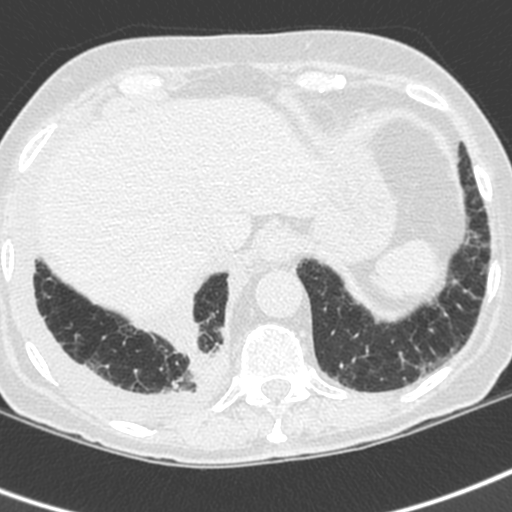
Low-dose screening chest CT, axial slice. Baseline screening round. Lung window (W 1500 / L -600 HU). Standard (soft-tissue) reconstruction kernel (C). Slice 159 of 192 in the series. Female, age 73 years at enrolment. Current smoker at enrolment.
Expert reader's lesion annotation, box from (x=161, y=328) to (x=235, y=406) px. The exam's reader record, not a measurement of the box and not confirmed to be the same lesion: non-calcified nodule or mass ≥4 mm, right lower lobe, 35 × 30 mm, spiculated (stellate) margins, soft tissue attenuation. Participant outcome: lung cancer diagnosed 22 days after this screen — adenocarcinoma, NOS, right lower lobe, stage IV (AJCC 6th edition), 35 mm at pathology.